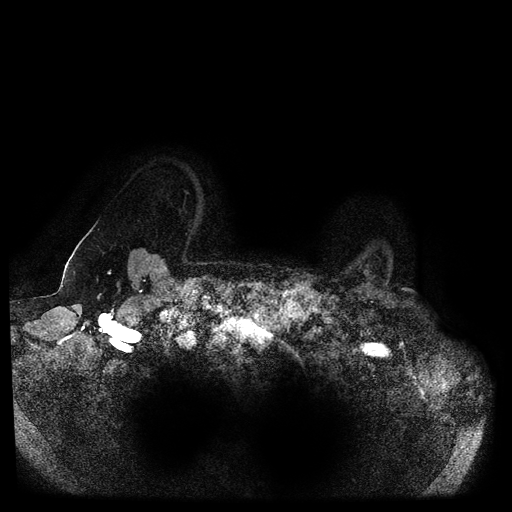
Breast MRI (dynamic contrast-enhanced, multi-phase), one axial slice; slice 92 of 116 in the series (ordered by position); dynamic contrast-enhanced series, time point 2 of 5 at this slice position (early post-contrast); 1.5 T; TE 2.6 ms, TR 5.3 ms; 512 × 512 image matrix, field of view 370 × 370 mm. Patient: female, 55 years.
Annotated regions visible in this slice (semi-automatic segmentation, software-assisted and operator-edited):
- breast lesion (labelled benign in the annotation): box from (x=362, y=266) to (x=372, y=279) px